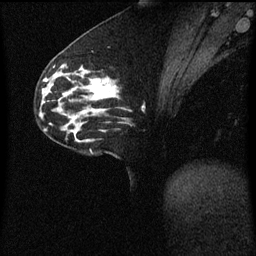
Breast MRI (dynamic contrast-enhanced), one sagittal slice; position 24 of 60 along the scan axis; dynamic contrast-enhanced series, image 2 of 3 at this slice position (ordered by acquisition); 1.5 T; TE 4.2 ms, TR 8.4 ms; 2 mm slice thickness; 256 × 256 image matrix, field of view 200 × 200 mm. Patient: female, 33 years. Case-level facts recorded for this patient, not image findings: setting: breast cancer imaged before/during neoadjuvant chemotherapy; receptor status: triple-negative.
Structures marked on this image (semi-automatic segmentation, software-assisted and operator-edited):
- analysis volume of interest (the breast-tissue region the enhancement analysis was run in; not a lesion): bounding box [x1, y1, x2, y2] px = [76, 66, 120, 113]
- tumour enhancement mask (voxels above the 70 % enhancement threshold inside the analysis volume of interest): [85, 78, 114, 99]